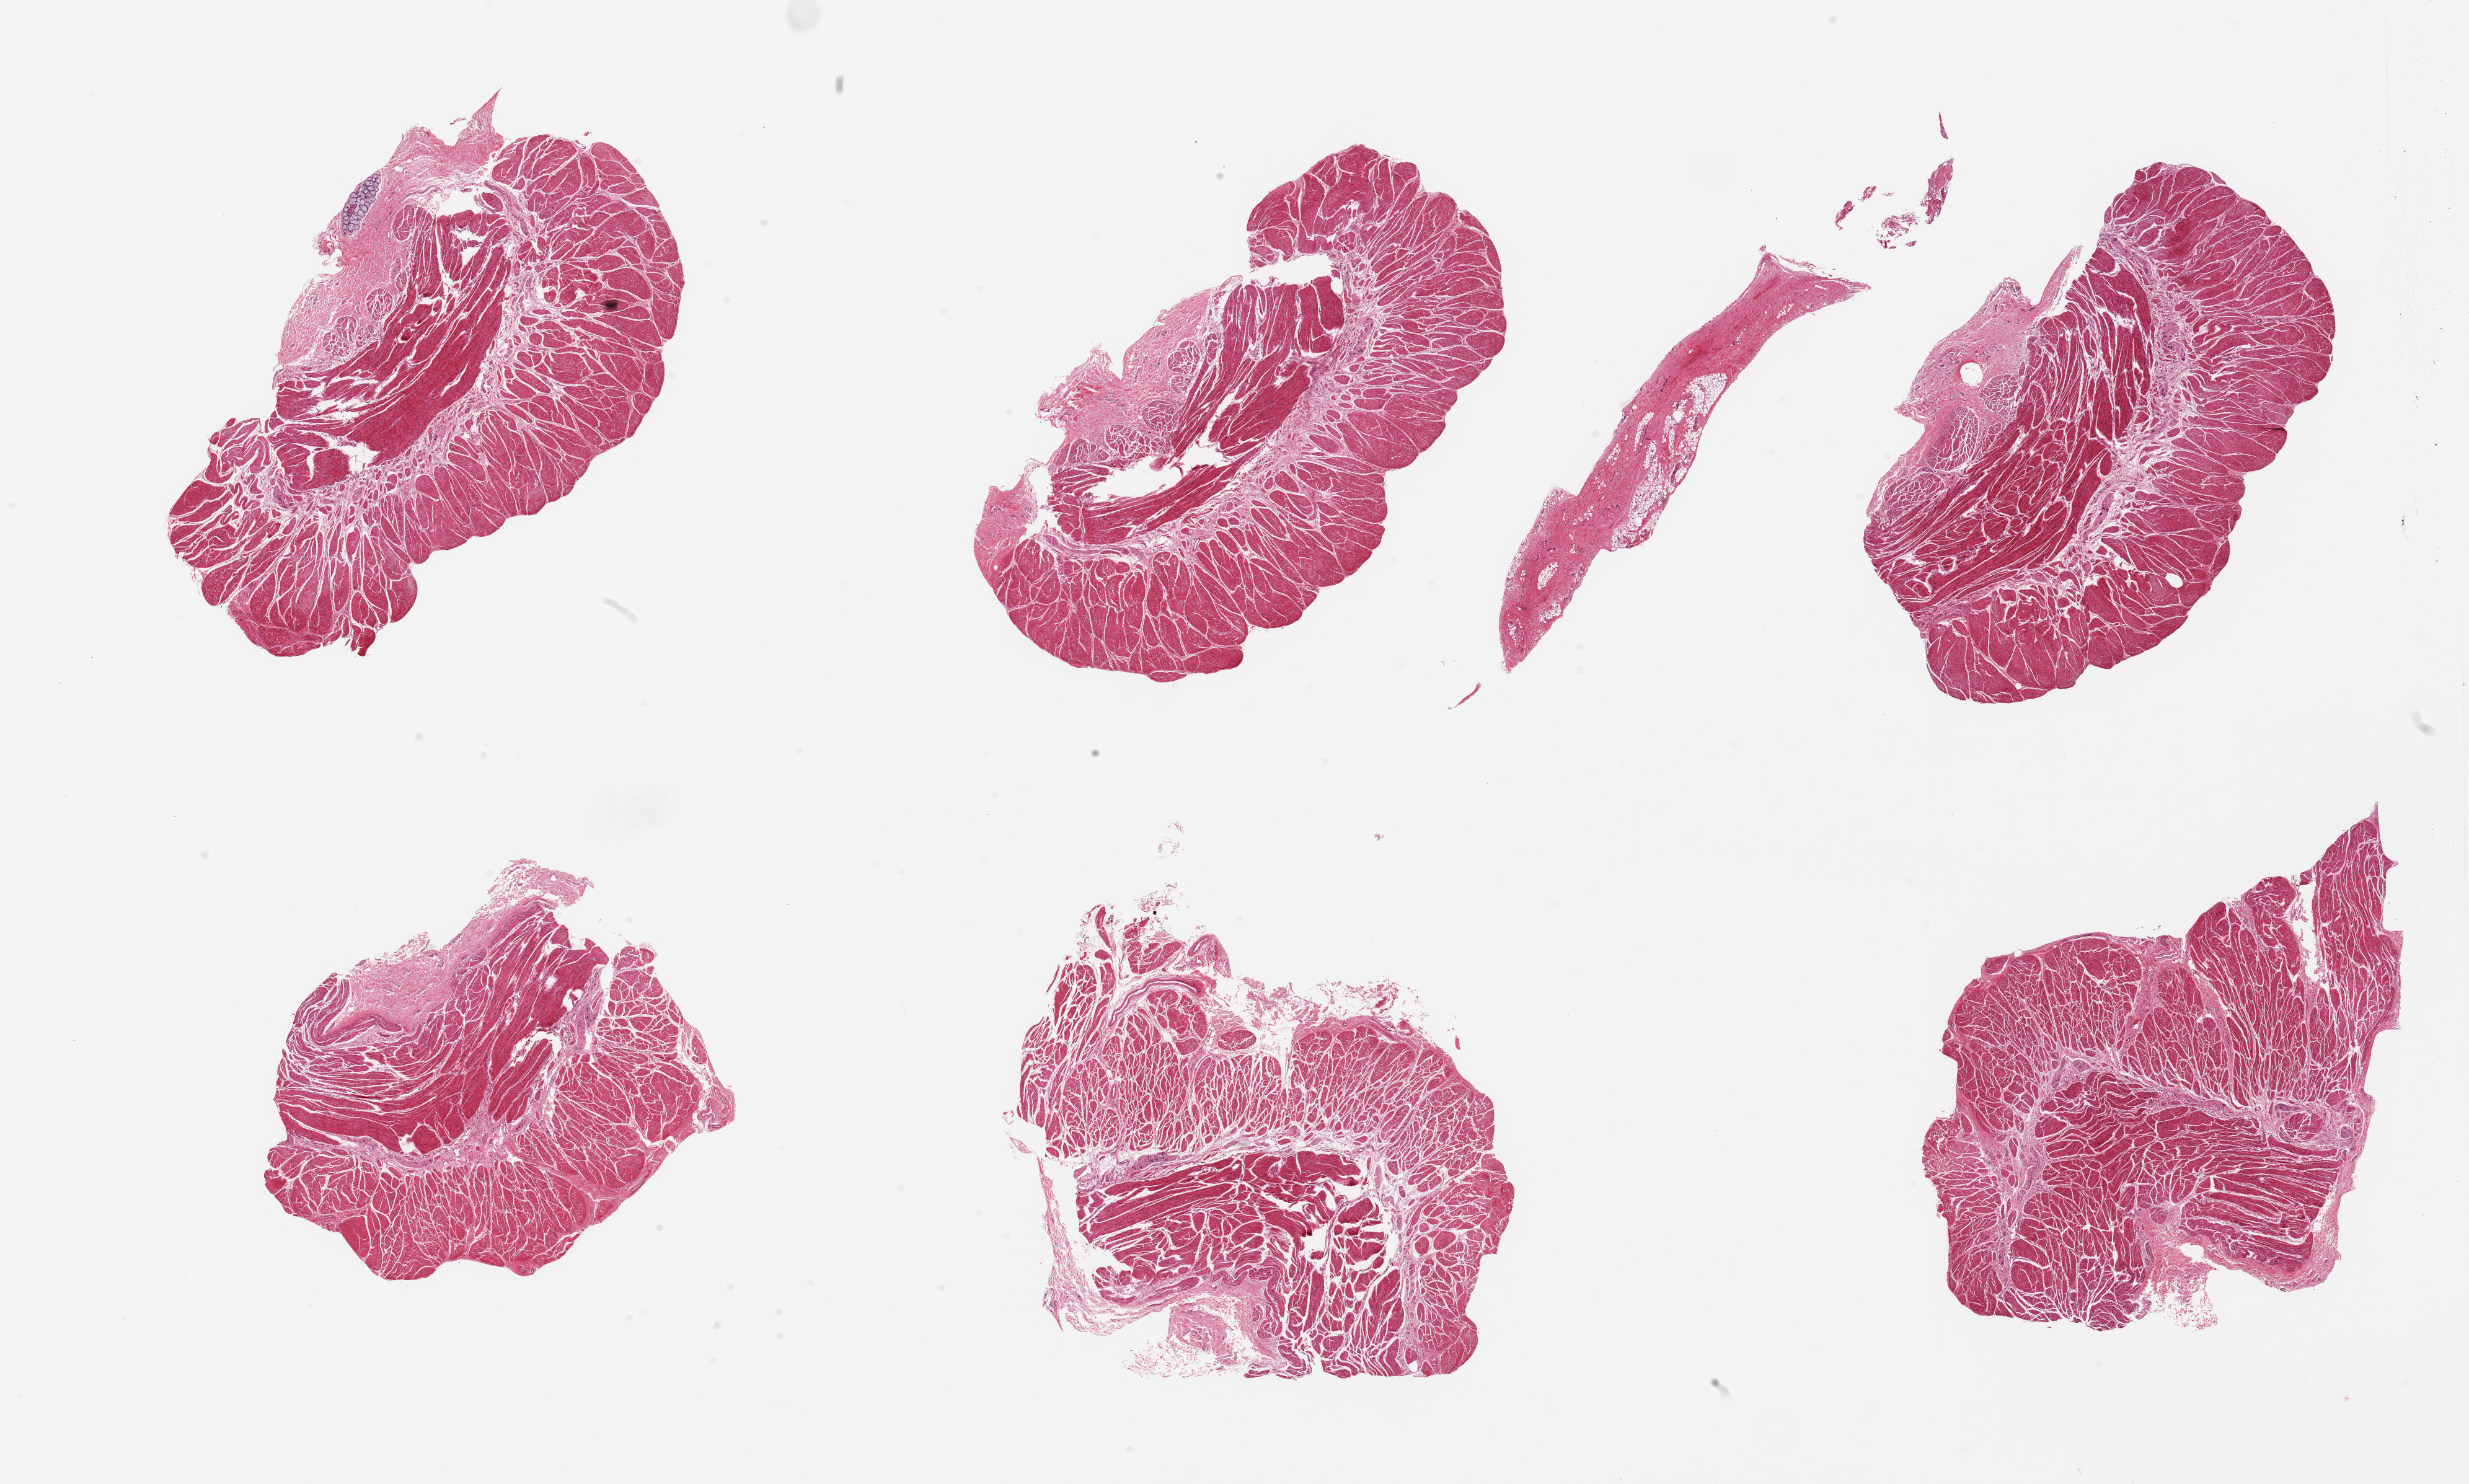
Whole-slide image, haematoxylin and eosin stain — low-resolution overview of the scanned area, about 31.5 x 18.9 mm (slide scanned at 20x). PAXgene-fixed, paraffin-embedded tissue. Section of esophageal muscle (target tissue). Tissue donor sample. Male donor.
Review note (as recorded): 6 pieces, all target muscularis; incidental mucus gland noted.